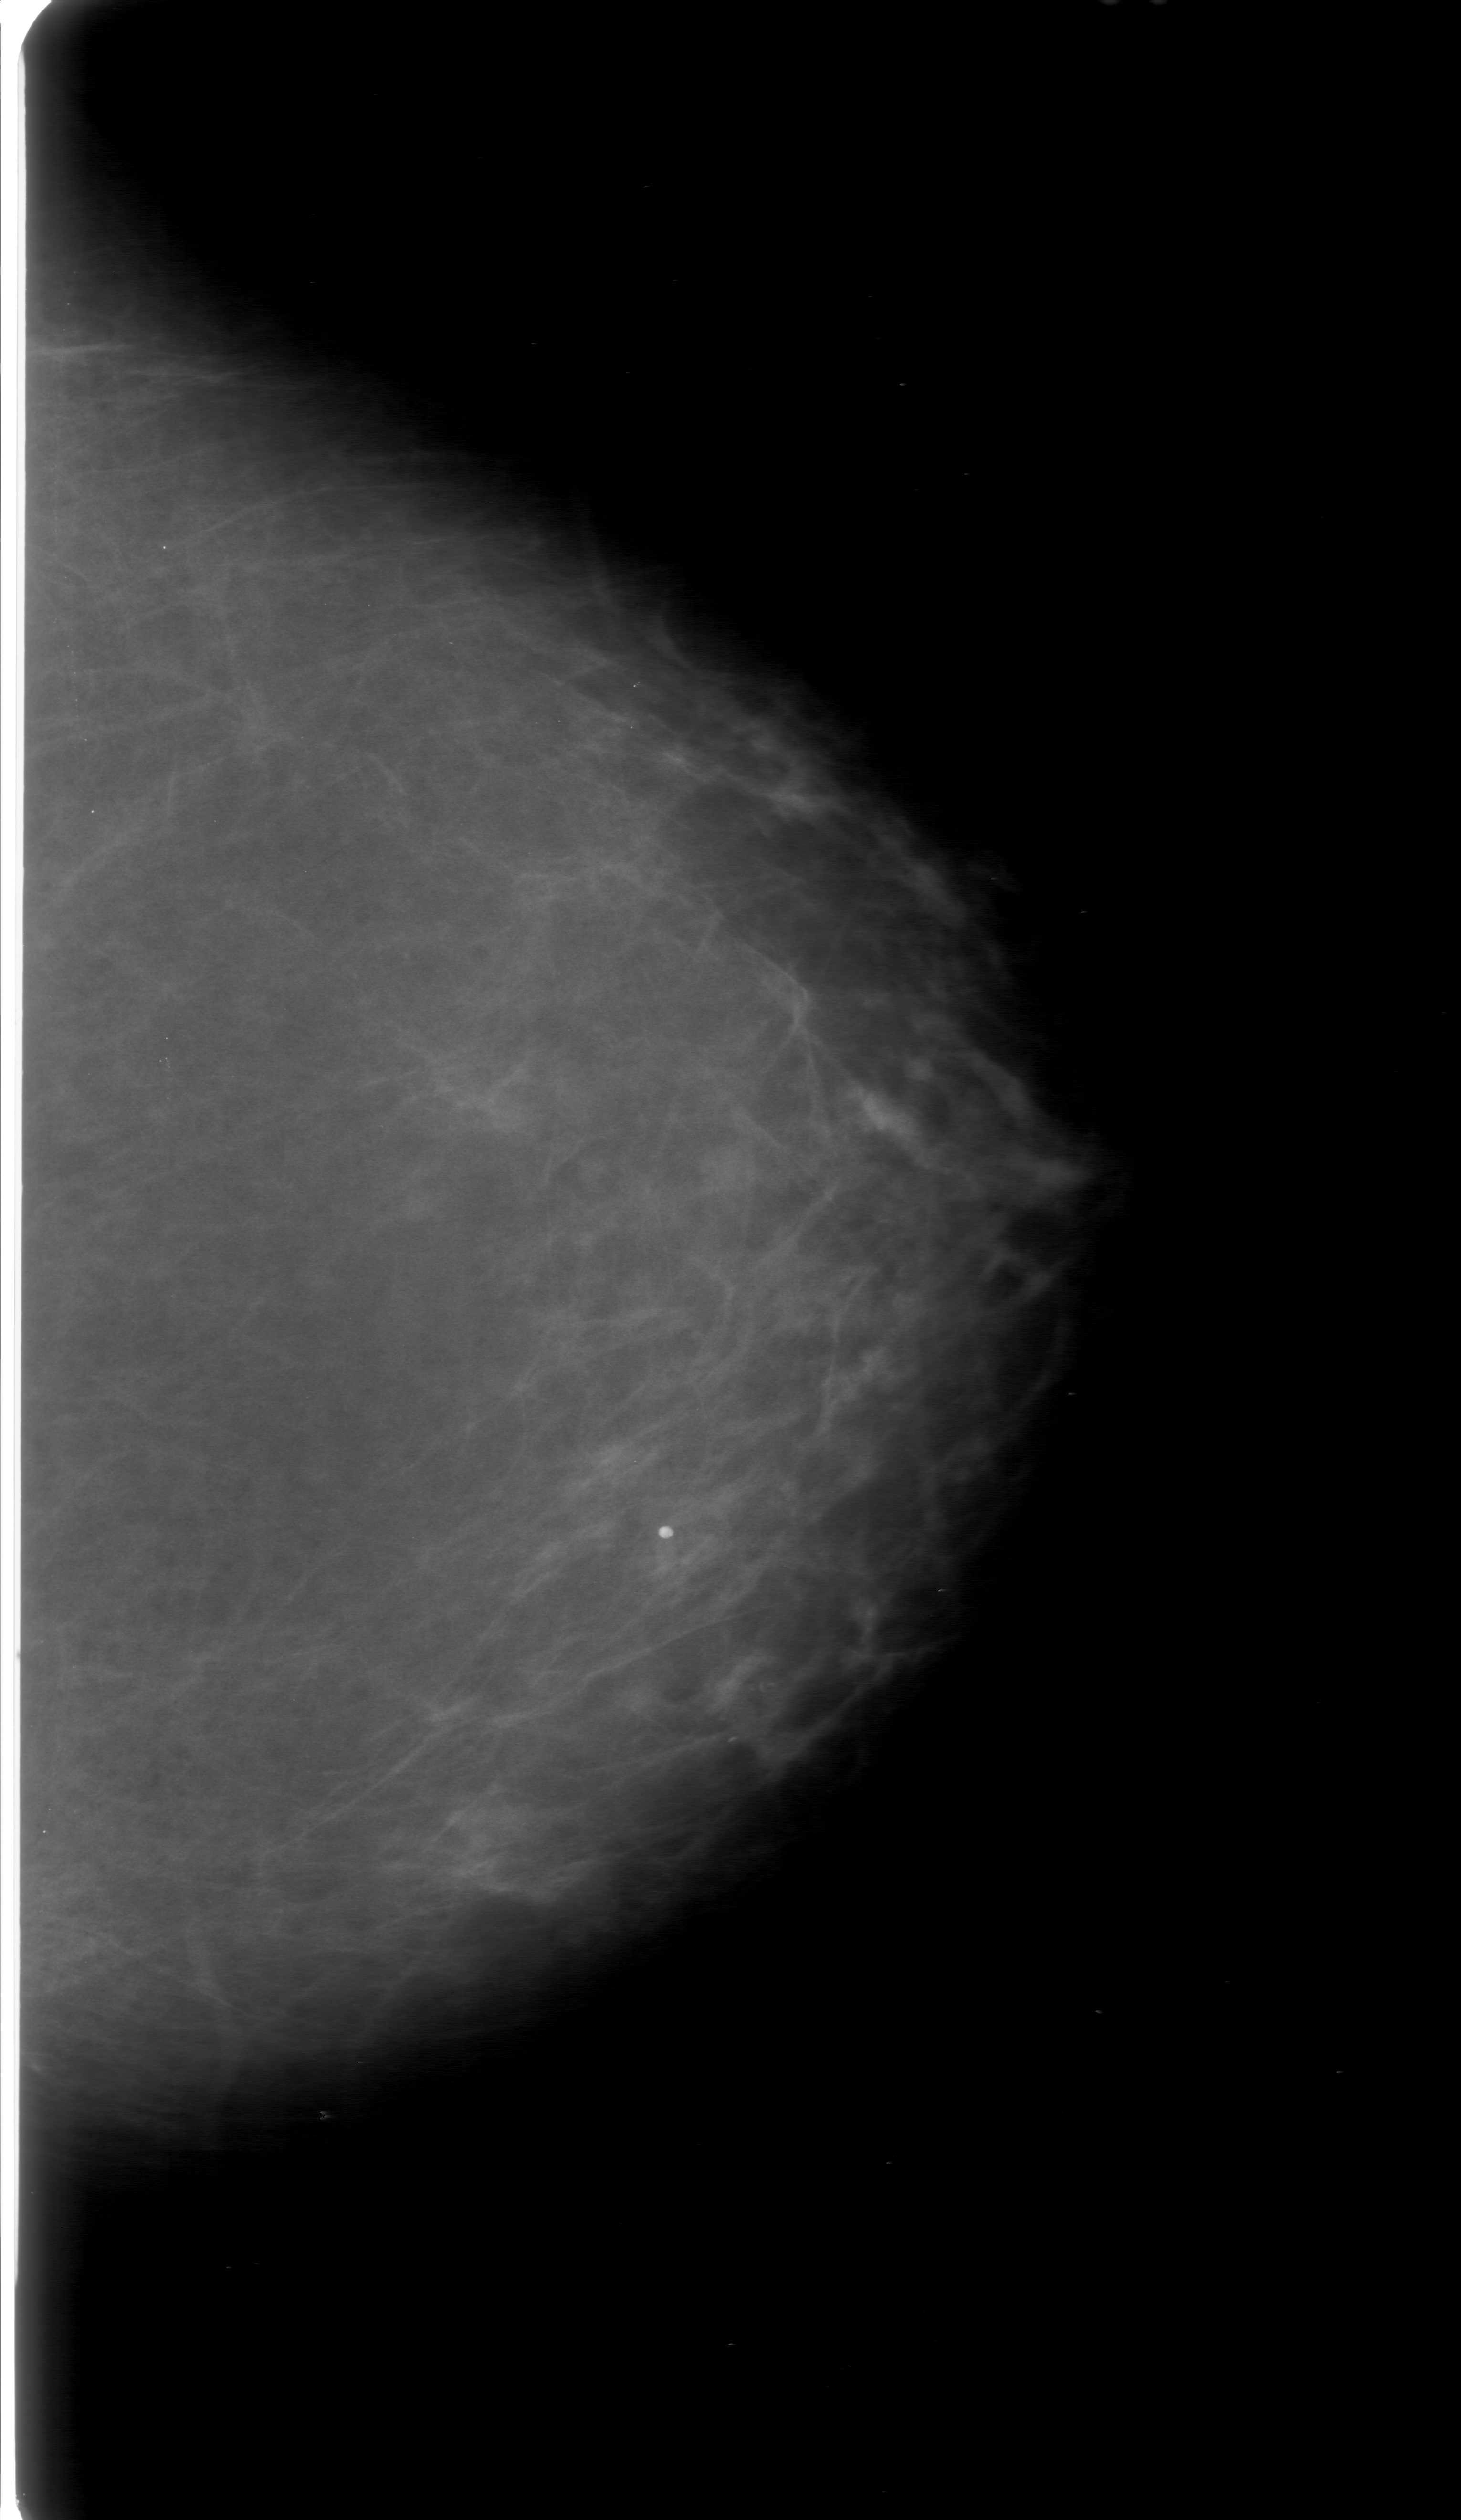
Mammogram (digitized film); left breast; CC view; BI-RADS breast density category 1 (scale 1–4).
Abnormality record for this image: calcifications, morphology fine linear branching, distribution clustered; BI-RADS assessment category 3; pathology result (as recorded, not read from the image): malignant.